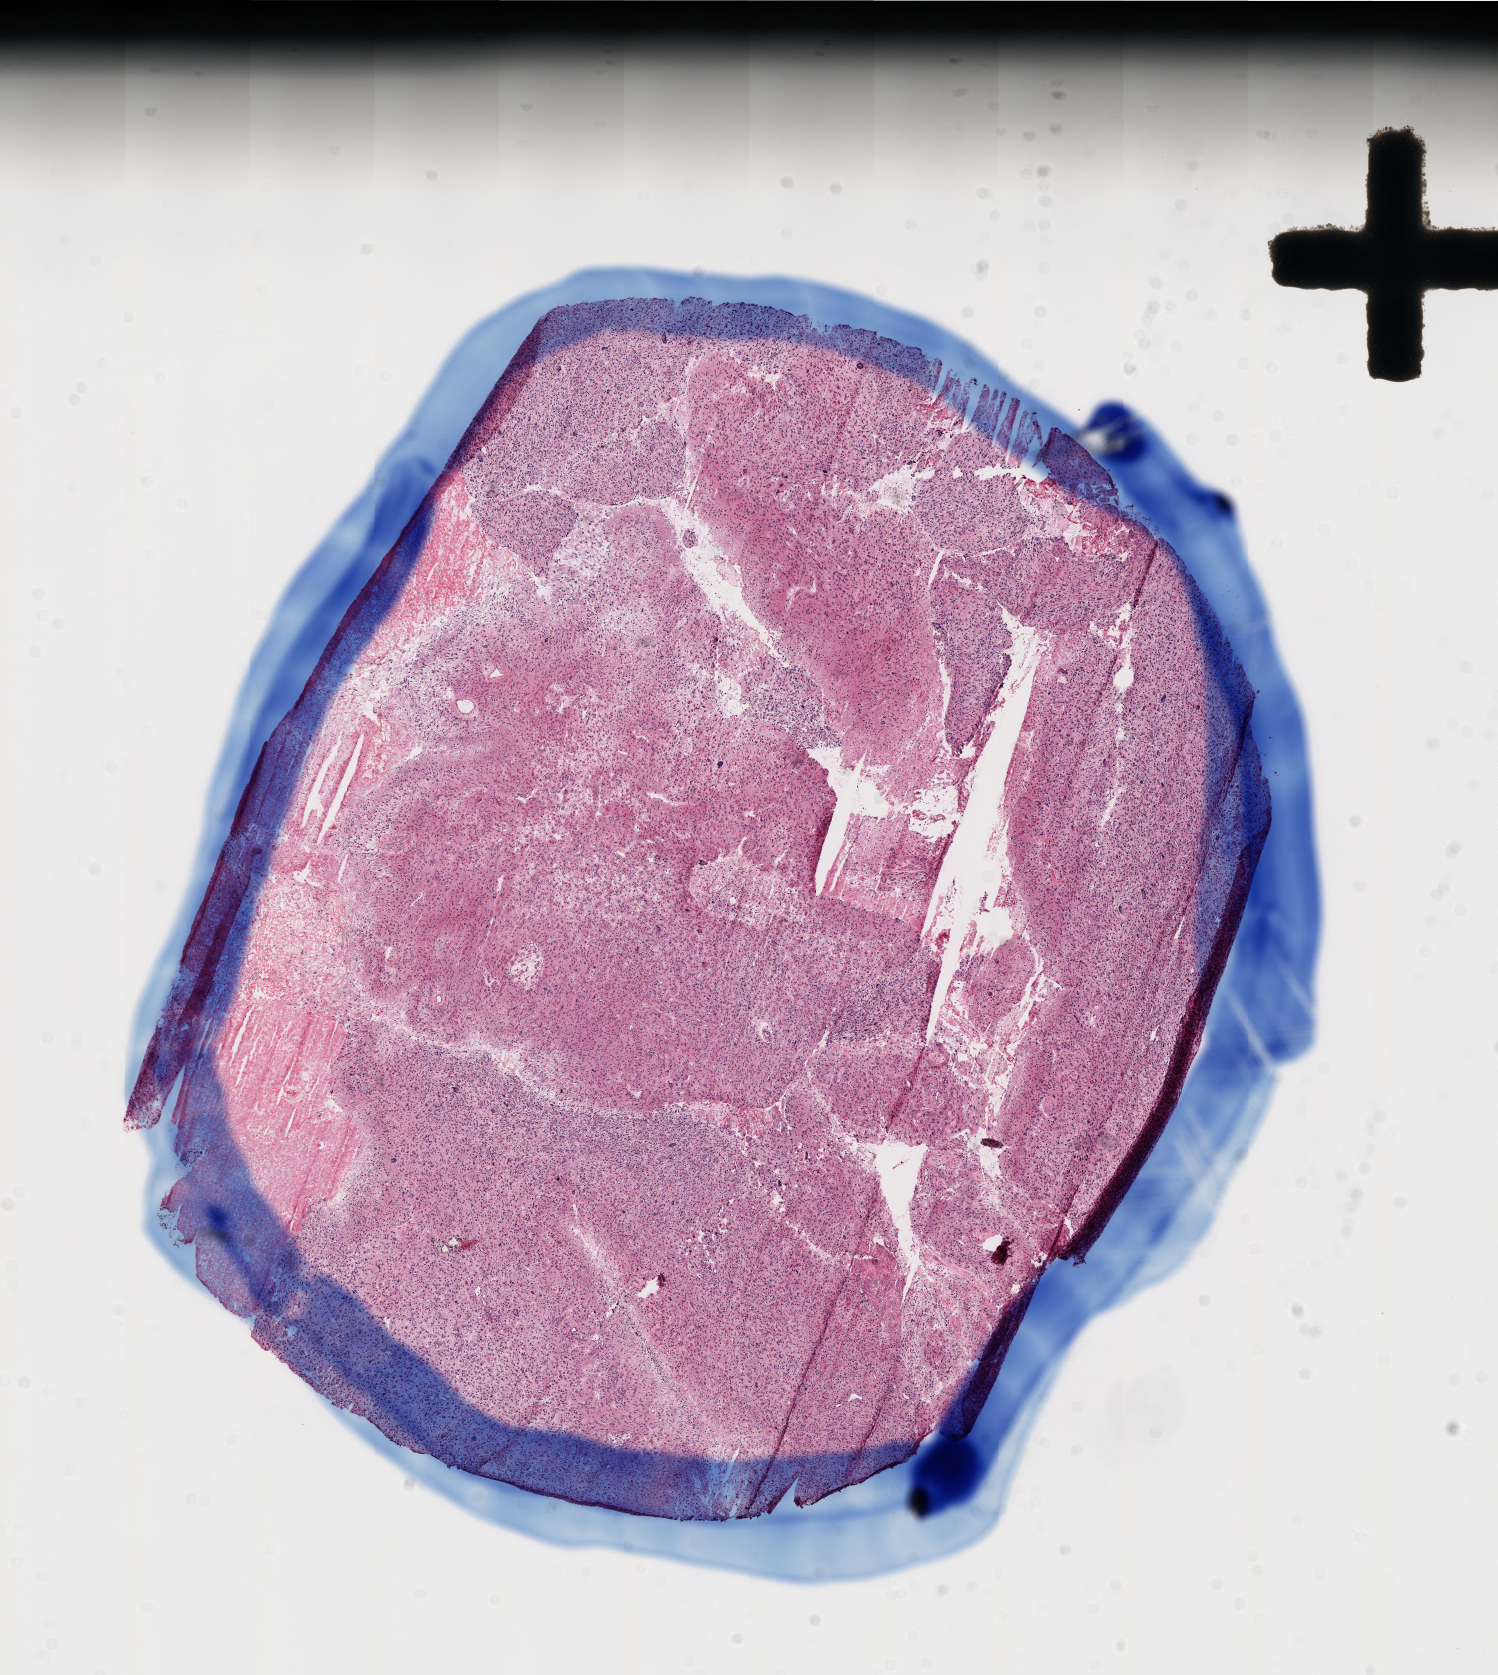
Digitized H&E tissue section (whole slide) — a low-resolution overview of the entire scanned area, about 12.0 x 13.4 mm (from a 20x scan); frozen section; primary tumour sample from the brain. Male patient; age at initial diagnosis 69 years. Composition of this section per pathologist review: tumour cells 90%, tumour nuclei 100%, normal cells 0%, stromal cells 0%, necrosis 10%.
Histologic diagnosis: Glioblastoma.